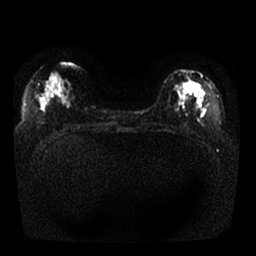
Breast MRI, one axial slice. Position 11 of 25 along the scan axis. Diffusion-weighted series; image 2 of 4 stored at this slice position (different b-values; order by instance number). 1.5 T. 4 mm slice thickness. 256 × 256 image matrix, field of view 330 × 330 mm. Female patient.
Annotated regions visible in this slice (manually delineated by an expert):
- tumour on diffusion-weighted imaging: bounding box (x1, y1, x2, y2) in pixels: (179, 76, 196, 95)